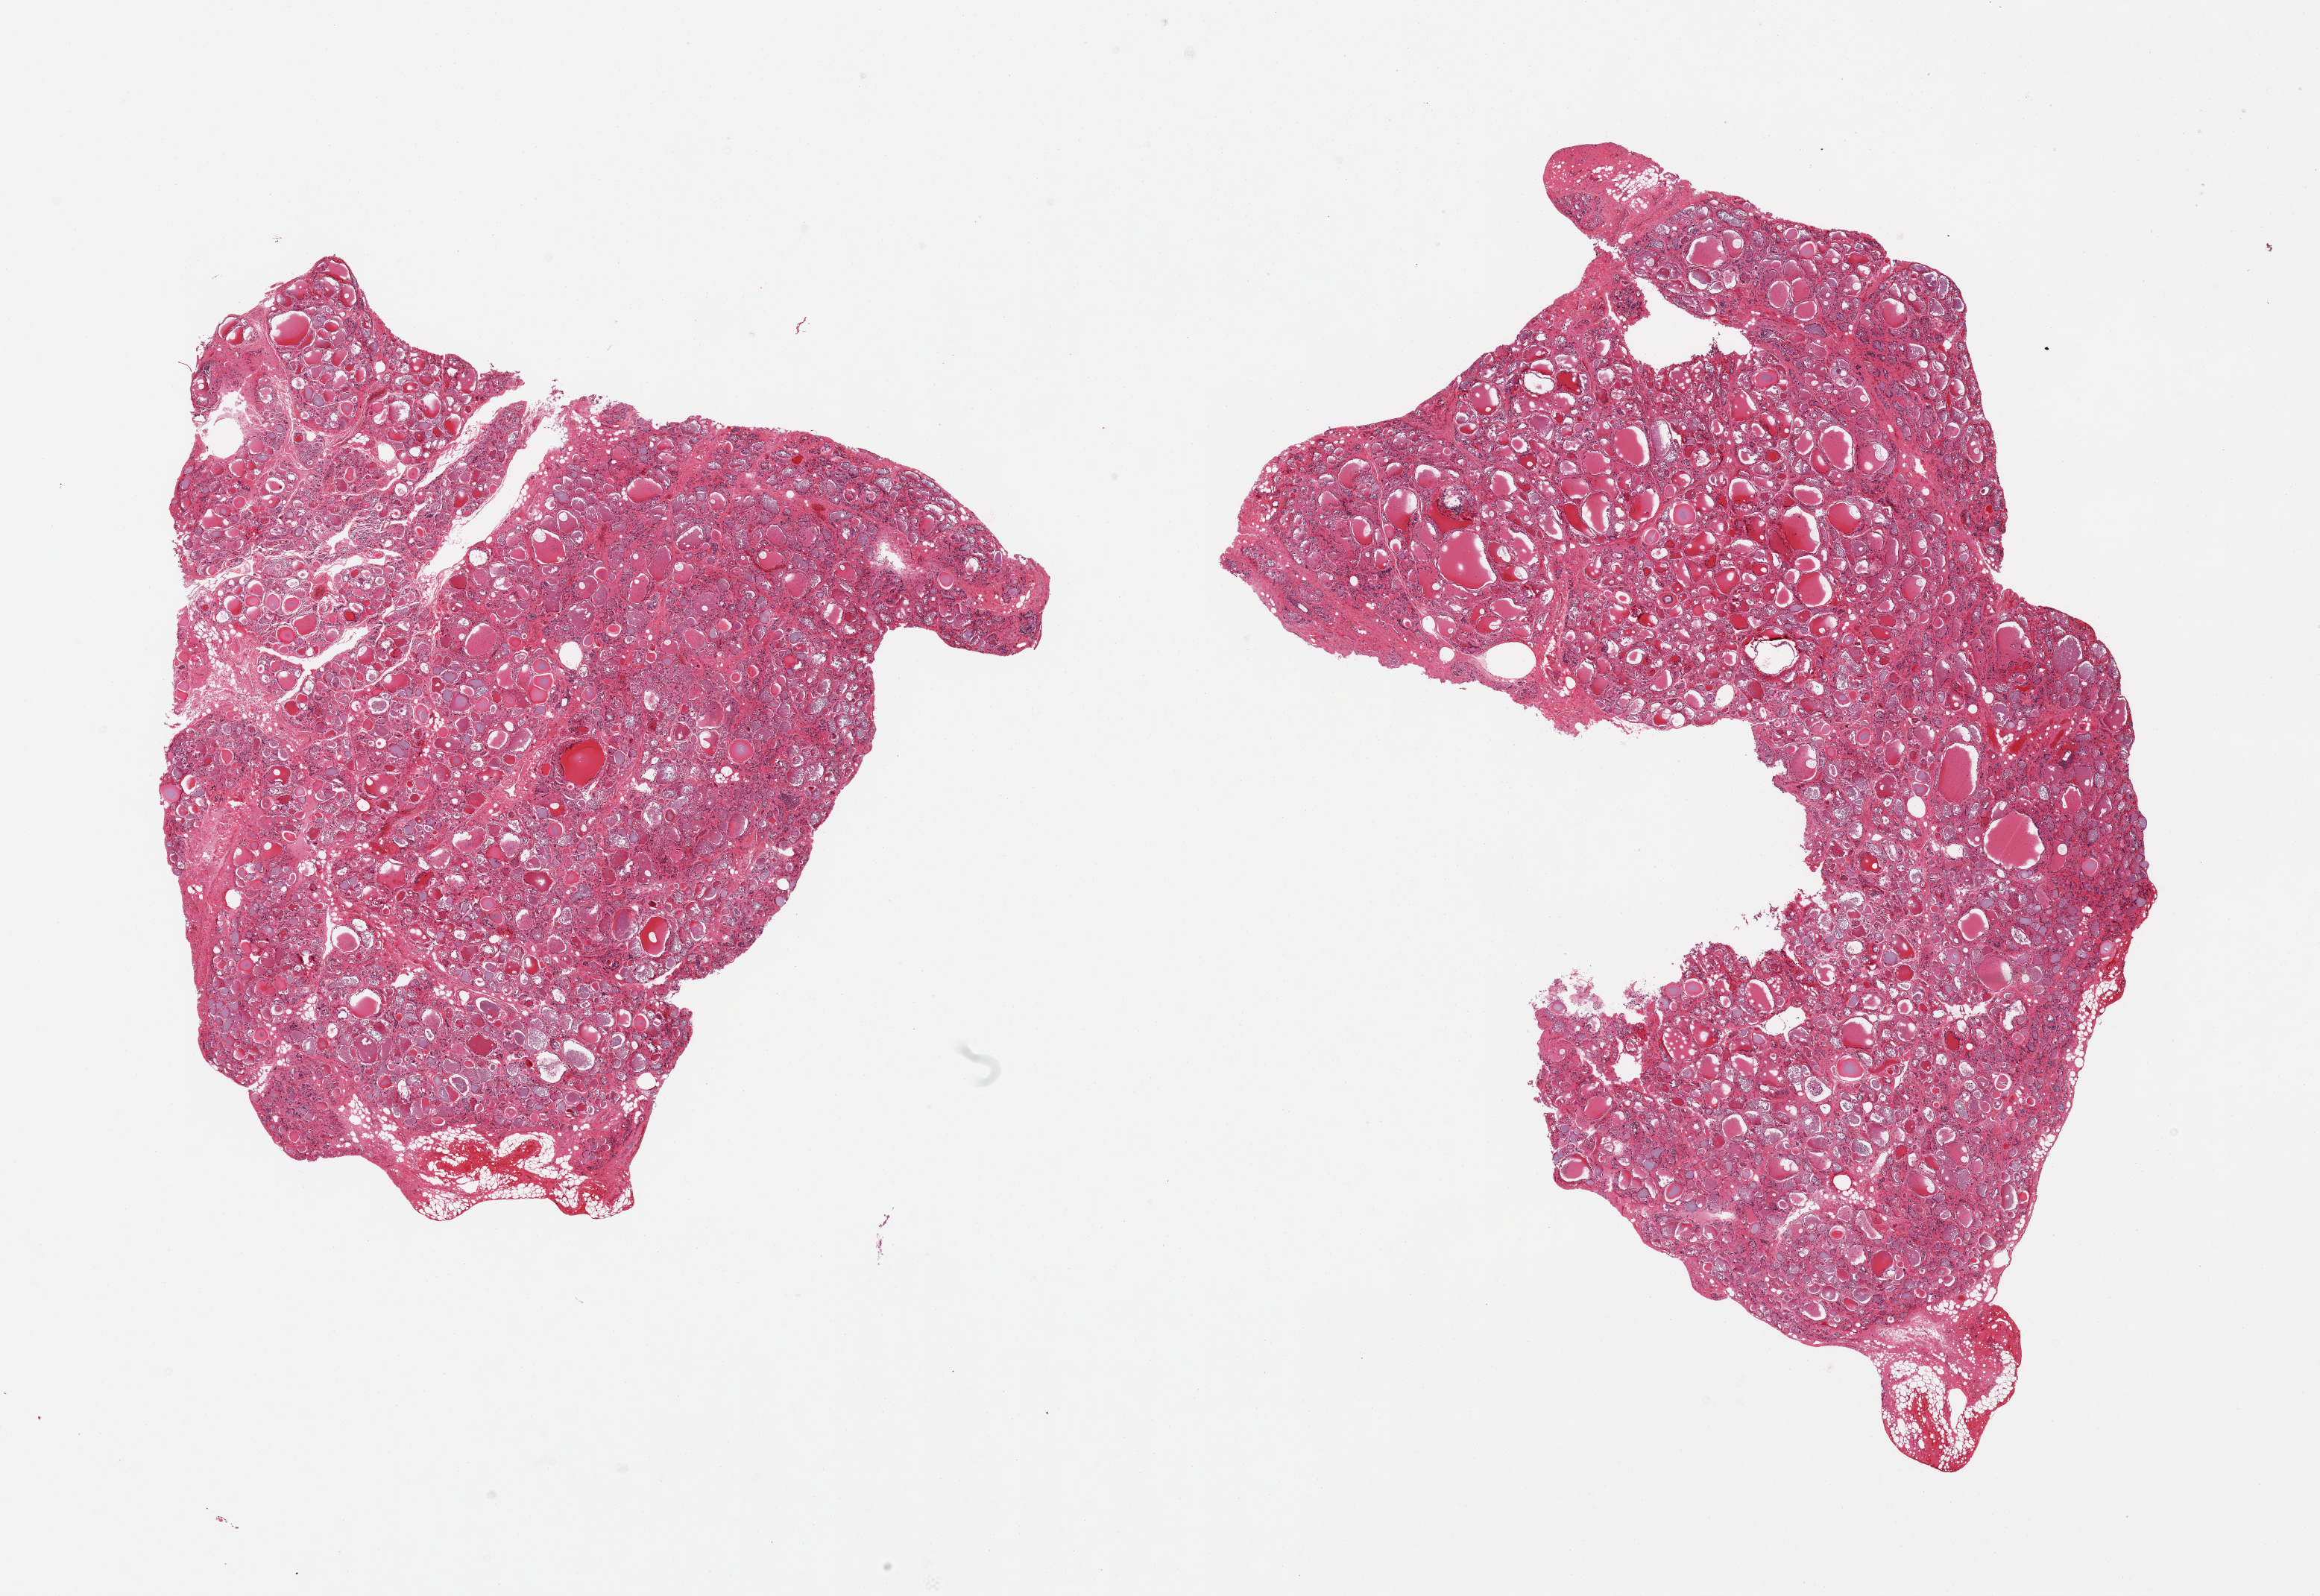
Whole-slide image, haematoxylin and eosin stain — whole scanned area (about 24.6 x 16.9 mm, from a 20x scan) shown as a low-resolution overview; PAXgene-fixed, paraffin-embedded tissue; target tissue: thyroid; tissue donor sample. Male donor.
Review note (as recorded): 2 pieces.